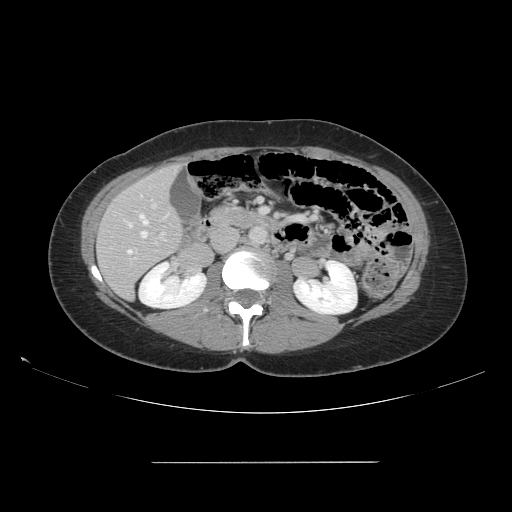
Contrast-enhanced abdominal CT, one axial slice; slice 63 of 151 in the series (ordered by position); intravenous contrast given; soft-tissue window (W 400 / L 40 HU); 512 × 512 image matrix, field of view 421 × 421 mm. Female patient, age 46 years. From the clinical record (not read from this slice): diagnosis: colorectal cancer liver metastases, imaged before liver resection; multiple liver metastases: yes; largest metastasis: 3 cm; disease in both lobes: yes.
Outlined on this slice (manually delineated by an expert):
- hepatic veins: bounding box <127,214,149,254> (left, top, right, bottom; pixels)
- liver: <98,166,182,298>
- planned liver remnant (the part of the liver to remain after resection): <98,166,182,298>
- portal vein (with intrahepatic branches): <130,200,165,260>